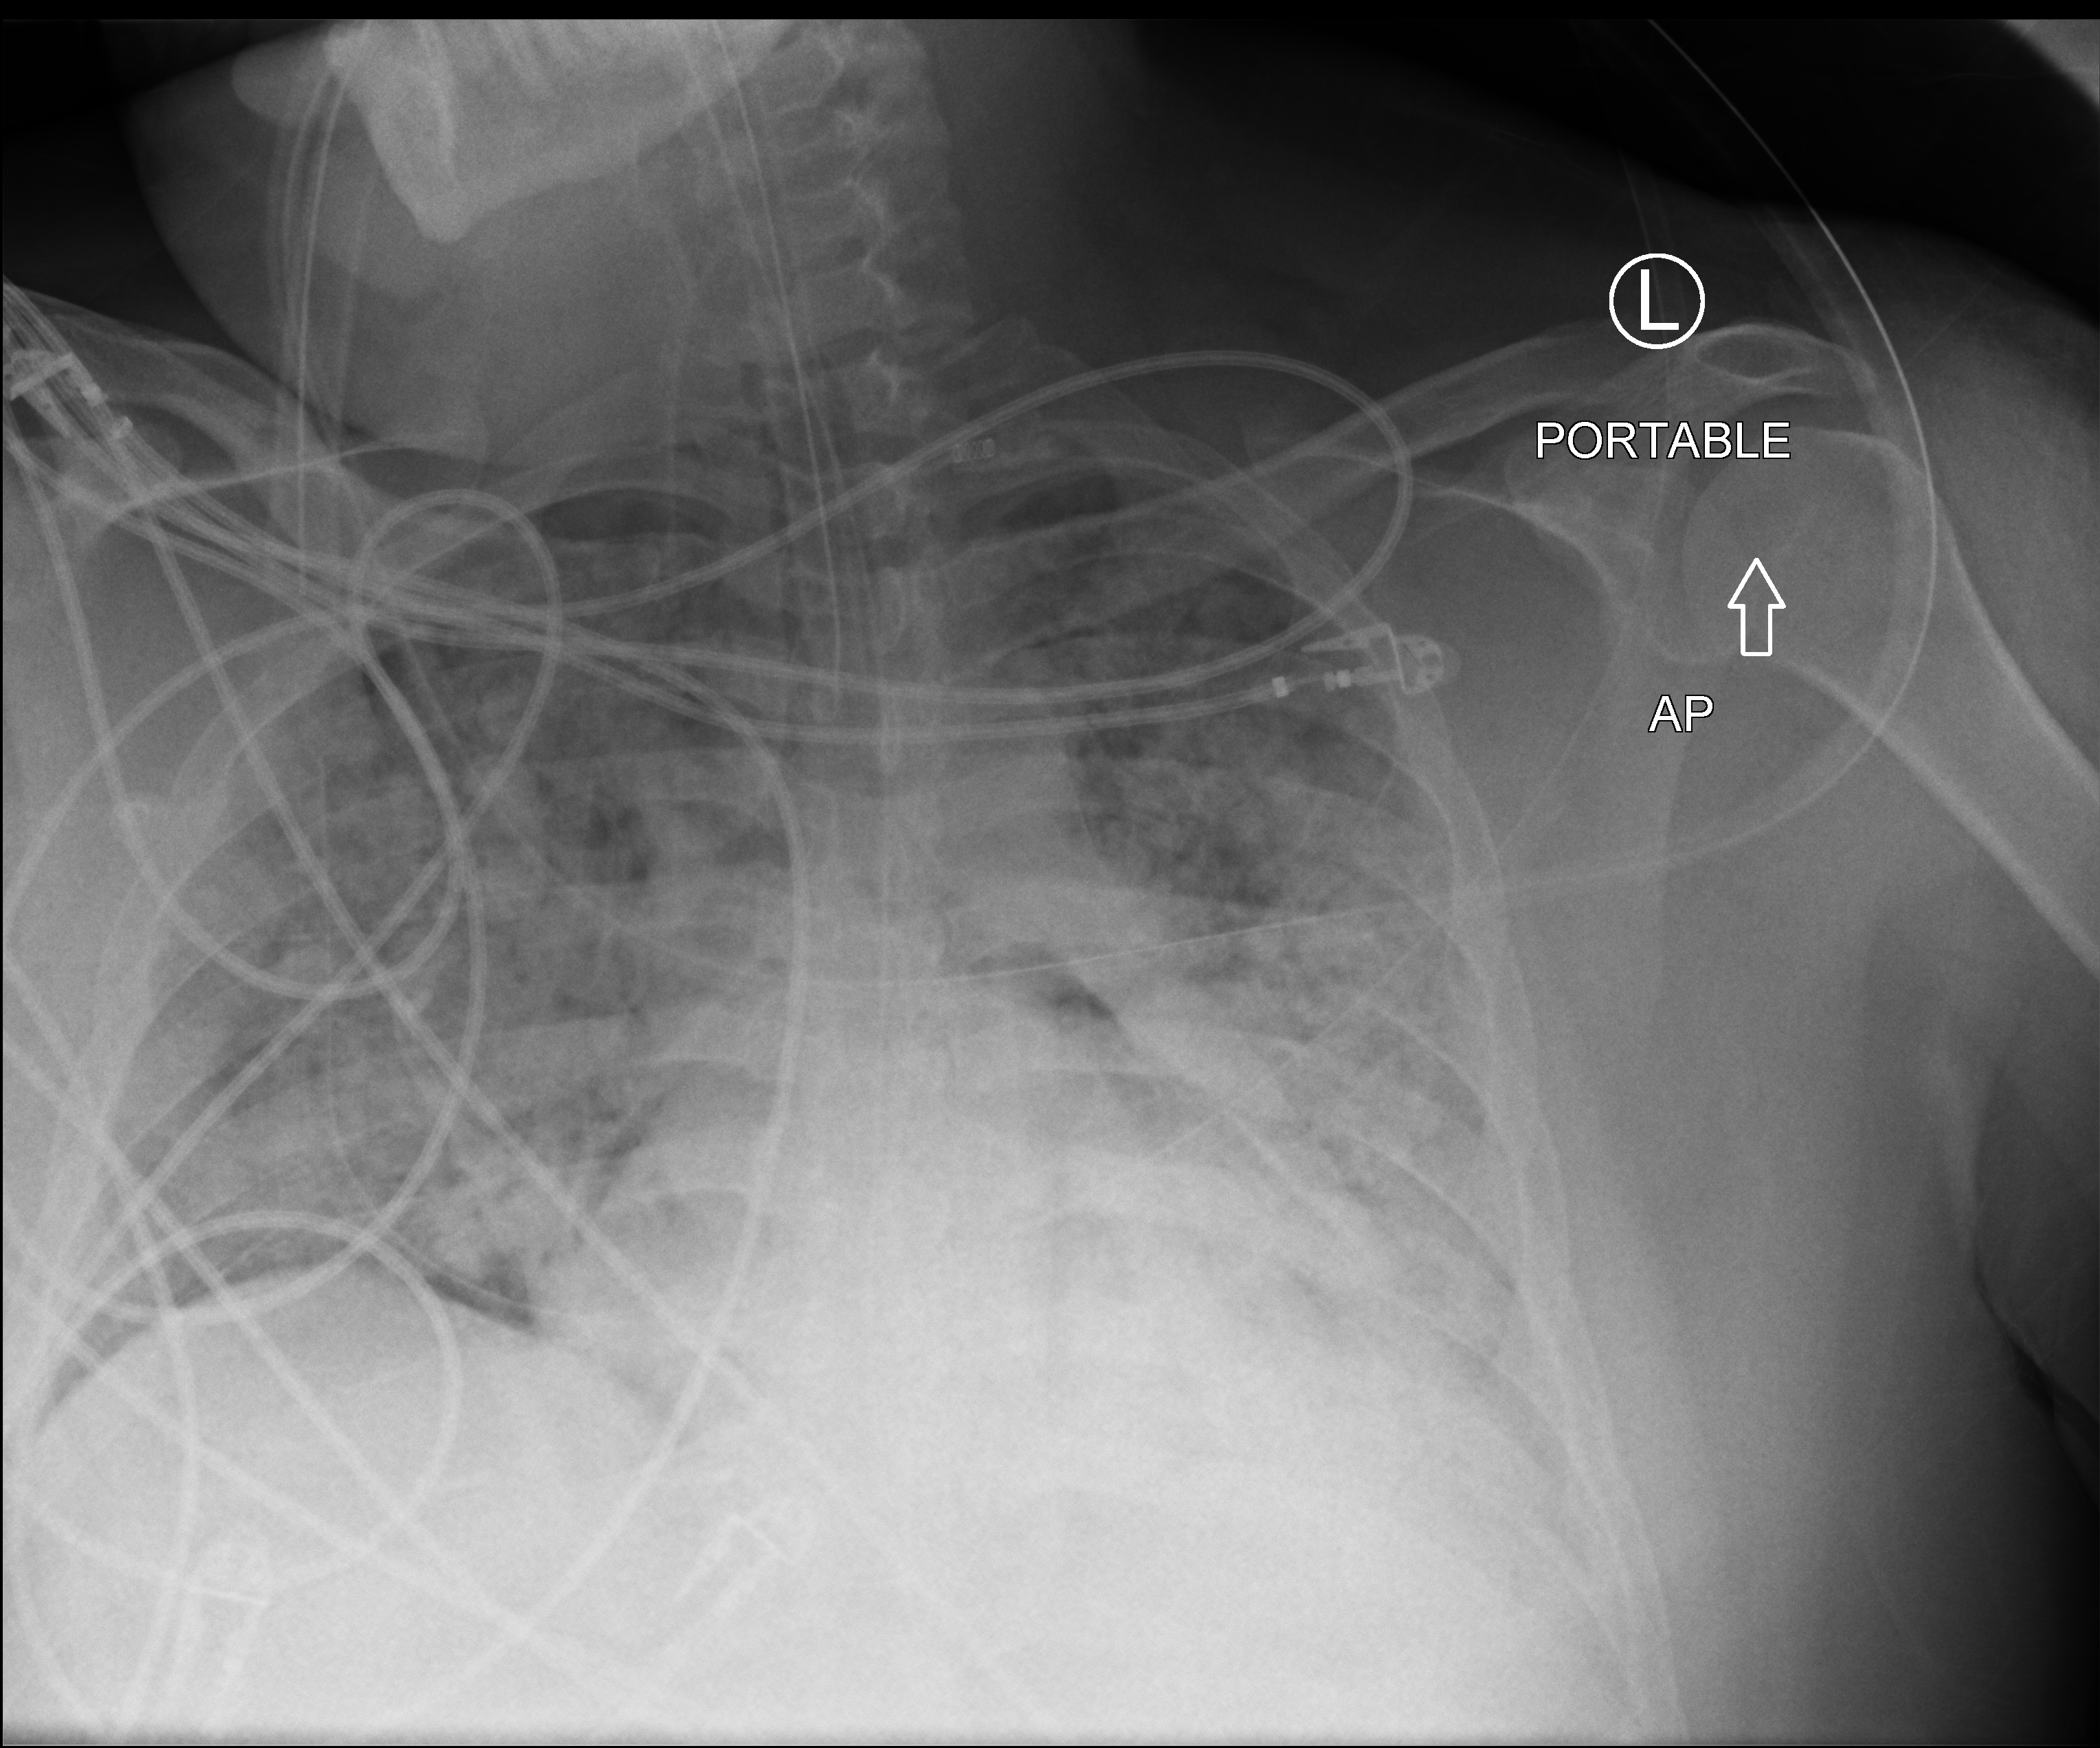
Bedside chest radiograph (computed radiography); anteroposterior (AP) projection. Patient hospitalised with COVID-19, aged 18–59 years.
From the hospital-stay record, not from the radiograph (when in the stay this image was taken is not recorded):
- admitted to intensive care during this hospital stay: yes
- chronic kidney disease (admission record): no